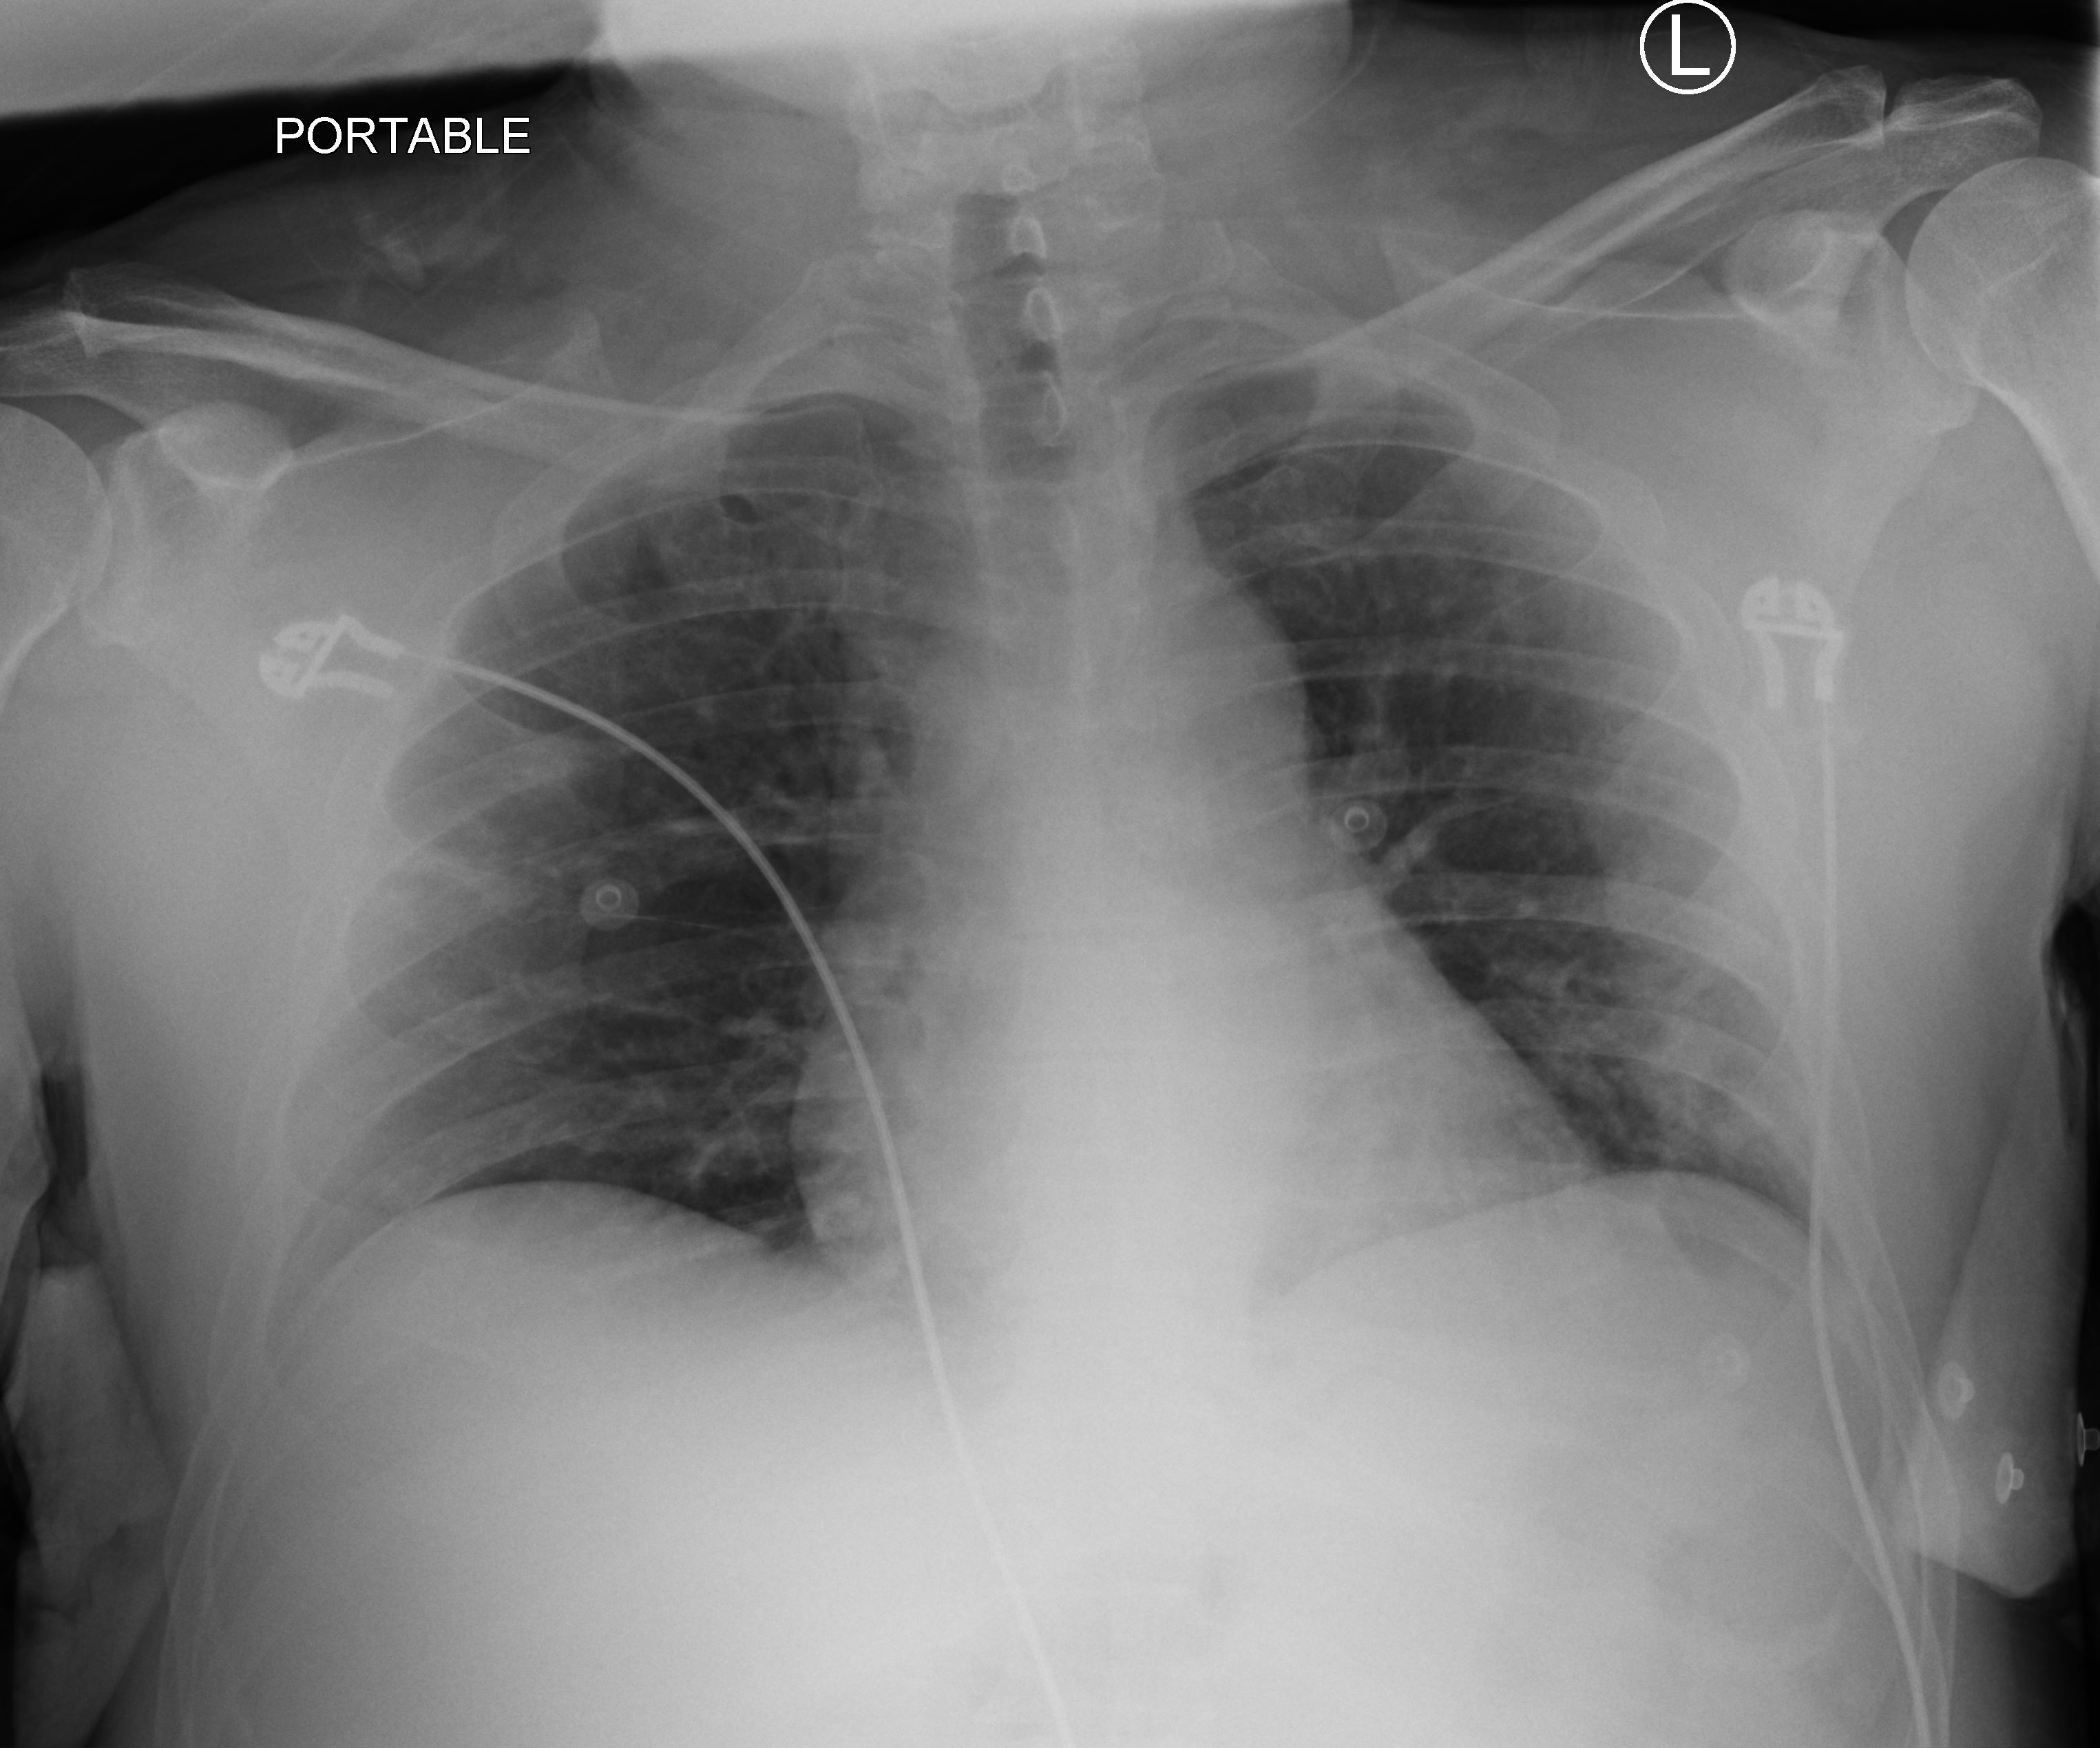
Bedside chest radiograph (computed radiography). Male patient hospitalised with COVID-19, age 18–59 years.
From the hospital-stay record, not from the radiograph (when in the stay this image was taken is not recorded): mechanically ventilated during this hospital stay: no; hypertension (admission record): no; smoking status (admission record): never.